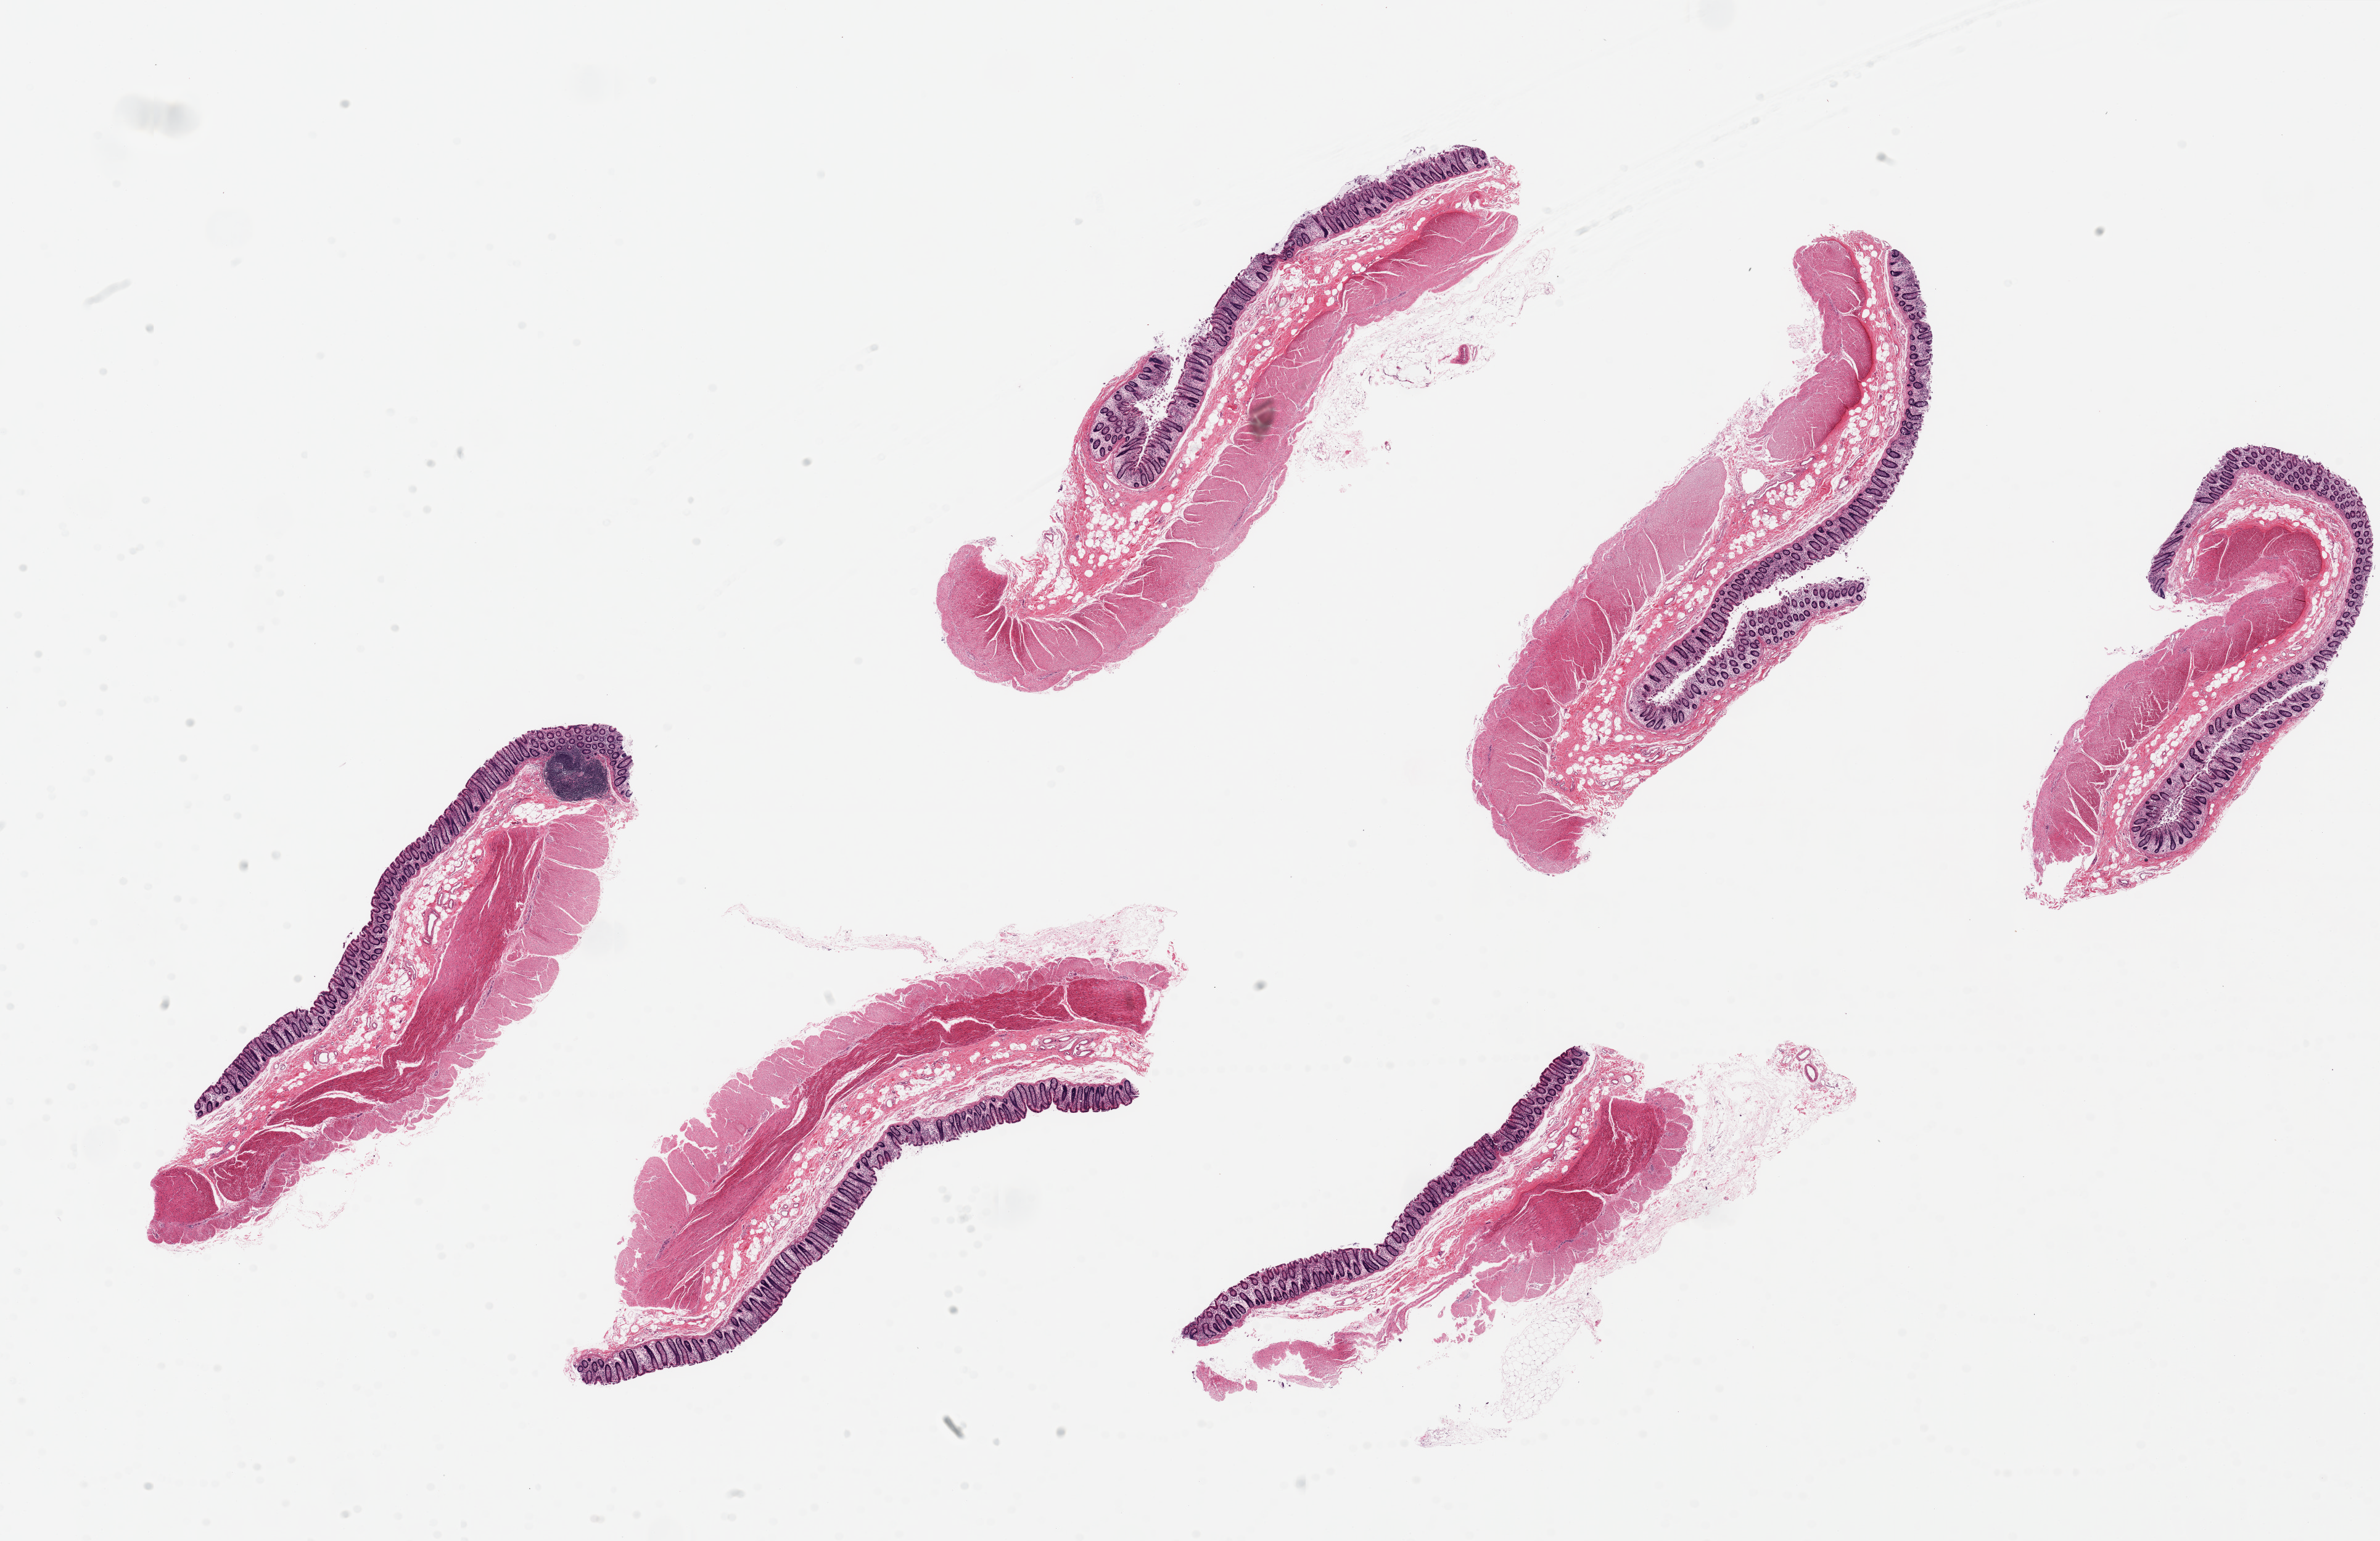
Whole-slide image, haematoxylin and eosin stain, shown as a low-resolution overview of the whole scanned area (about 30.5 x 19.8 mm, from a 20x scan); PAXgene-fixed, paraffin-embedded tissue; section of transverse colon (target tissue); tissue donor sample. Donor sex: male.
- review note (as recorded): 6 pieces, up to 10x4mm; Good mucosal preservation